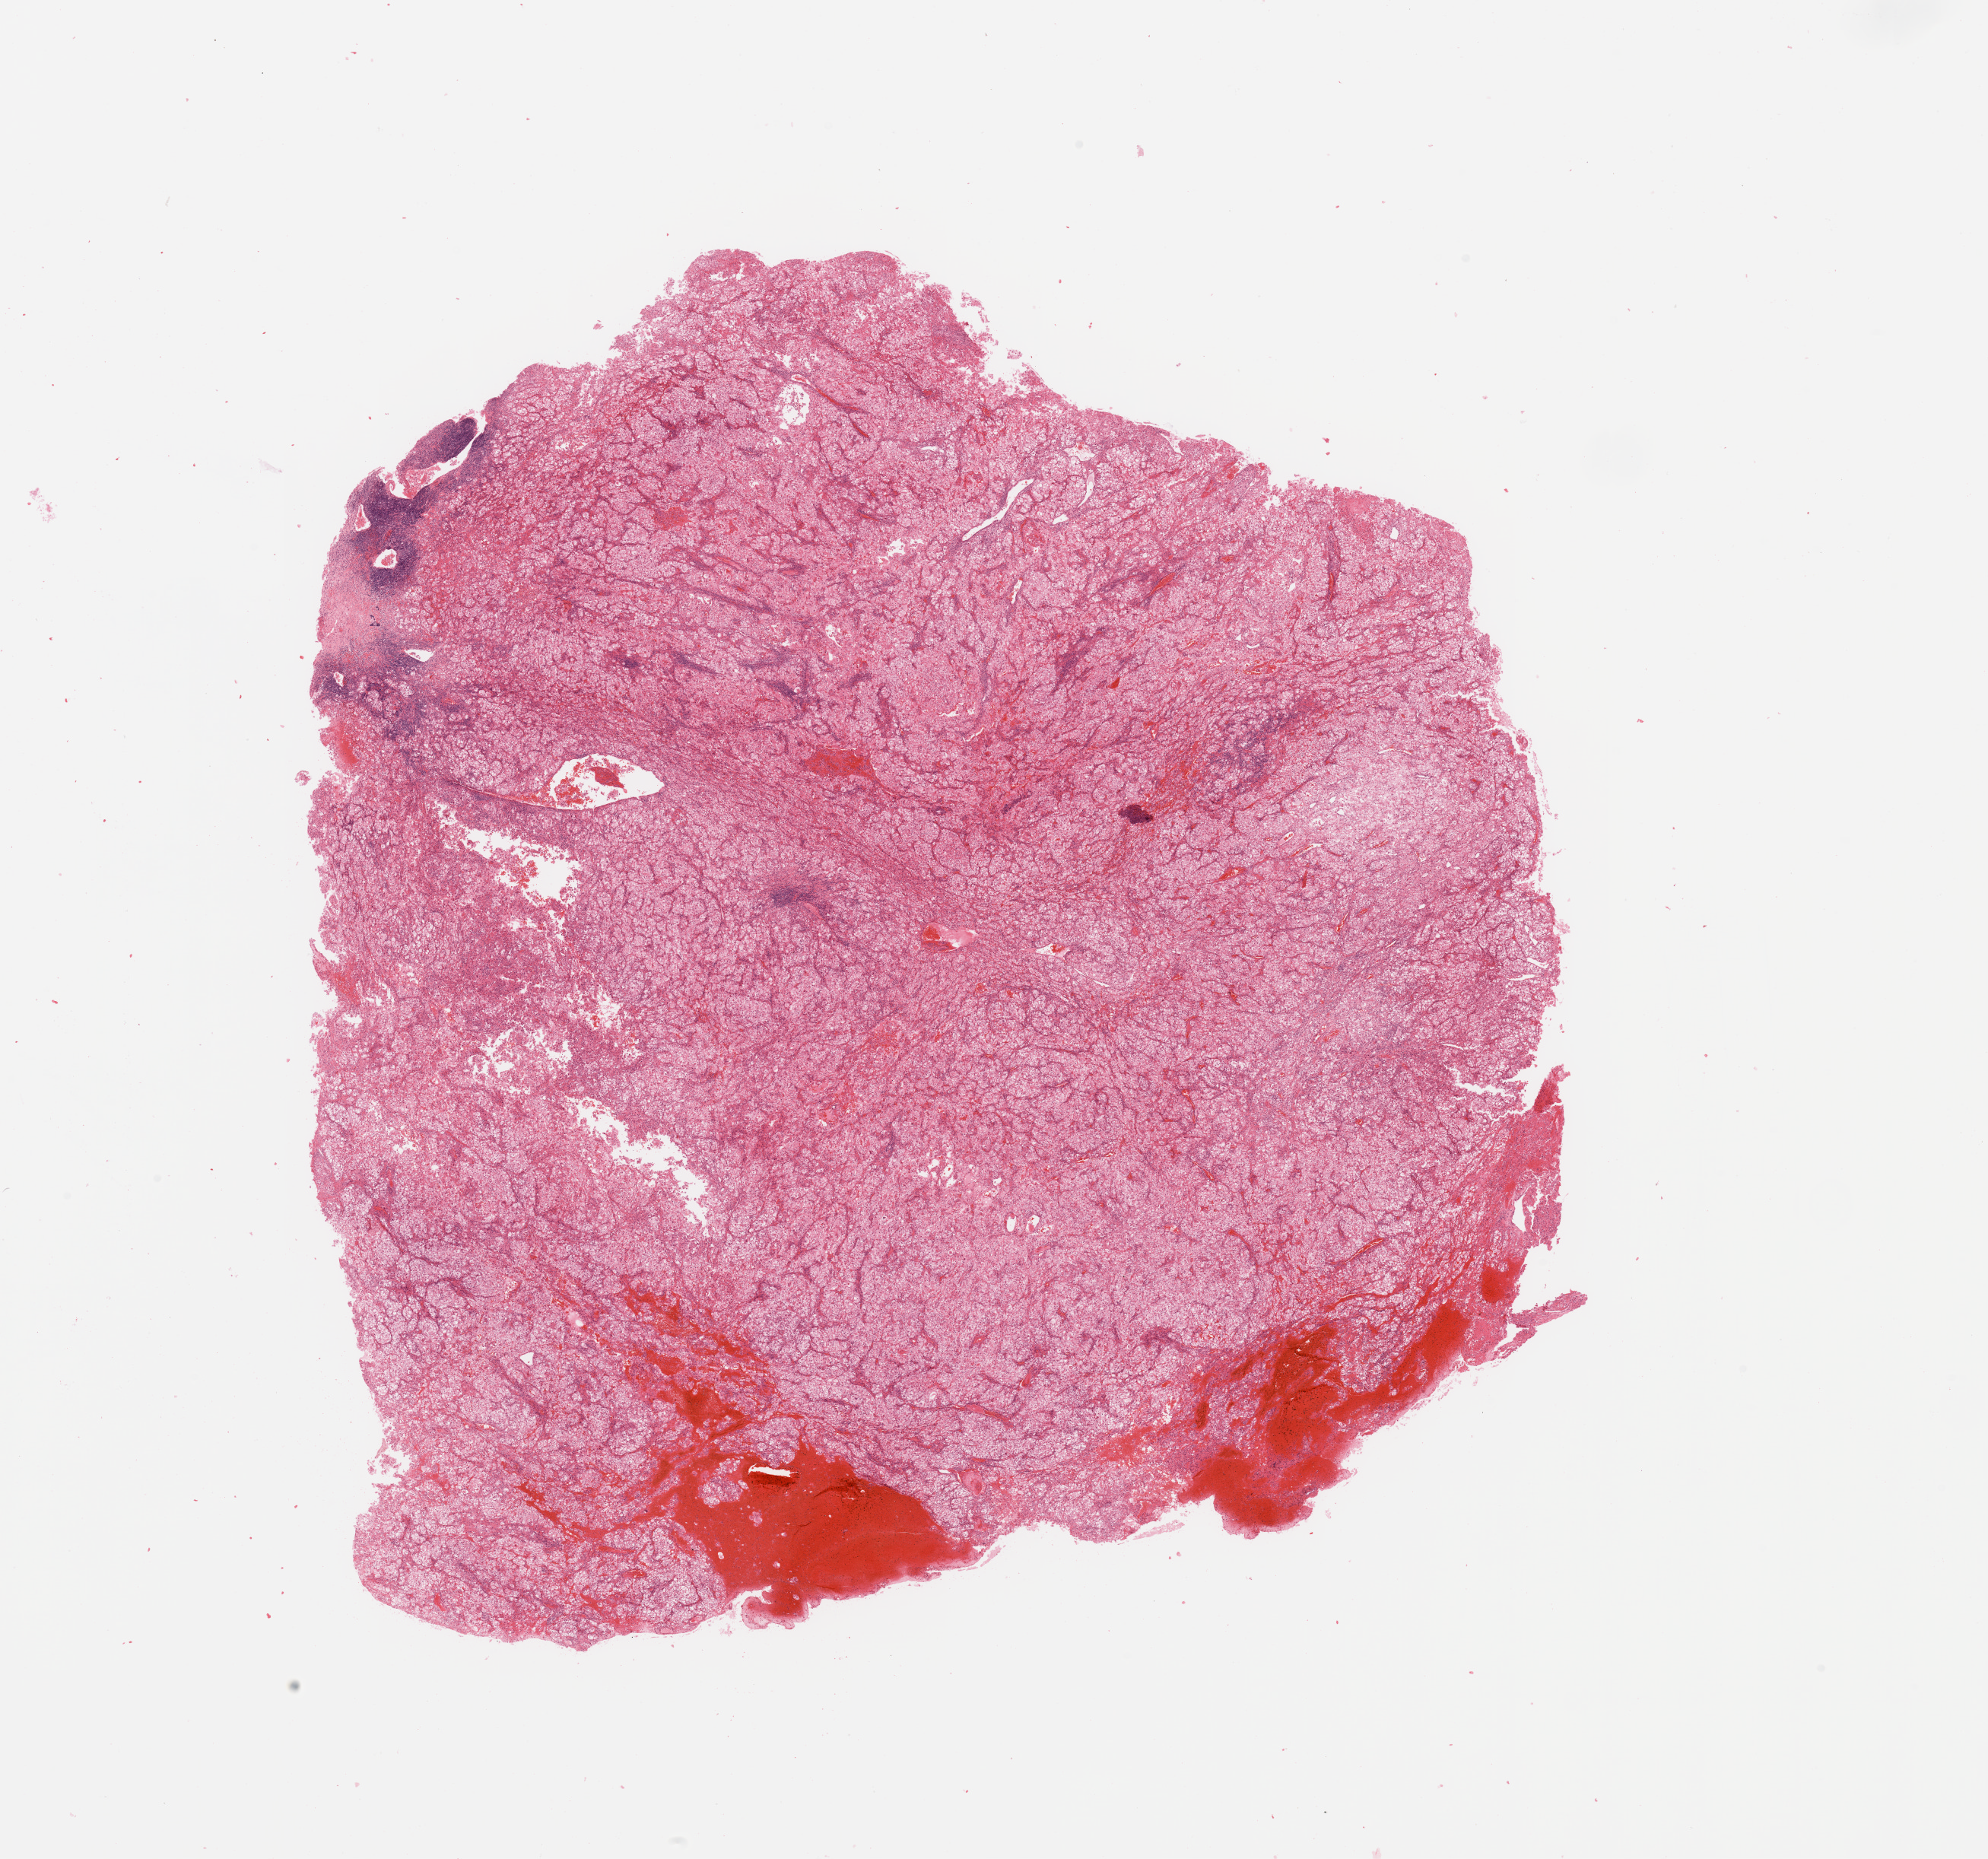
H&E-stained whole-slide image, shown as a low-resolution overview of the whole scanned area (about 20.7 x 19.3 mm, from a 20x scan). Tumour tissue sample, sampled site: kidney. 68-year-old male patient. Histologic grade: G3 (poorly differentiated). Composition of this section per pathologist review: tumour nuclei 85%, necrosis 5%.
• AJCC pathologic stage: II
• diagnosis: Renal cell carcinoma, NOS